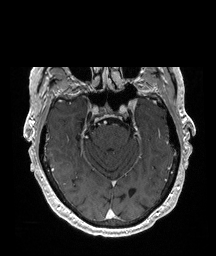
Brain MRI from a brain-tumour surgery series, one axial slice. Position 142 of 208 along the scan axis. T1-weighted post-contrast. 1 mm slice thickness. 216 × 256 image matrix, field of view 216 × 256 mm. Case-level facts recorded for this patient, not image findings: histopathology: Glioblastoma; WHO grade: 4; IDH mutation: no; tumour location: Right Temporal.
Outlined on this slice (manually delineated by an expert):
- tumour: bounding box [x1, y1, x2, y2] px = [50, 161, 60, 171]